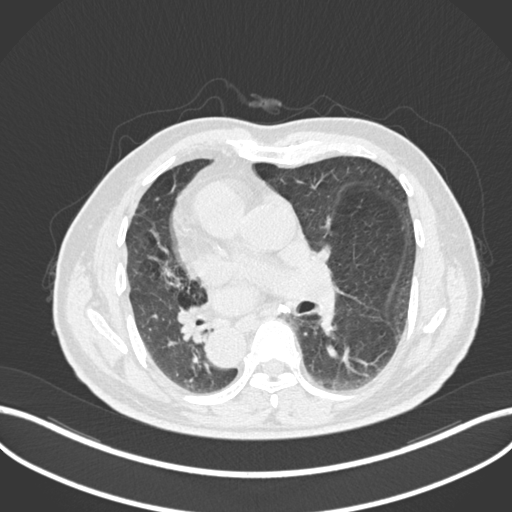
Chest CT, one axial slice. Position 111 of 206 along the scan axis. 120 kVp. Lung window (W 1500 / L -600 HU). 1 mm slice thickness. 512 × 512 image matrix, field of view 400 × 400 mm. Male patient, age 67 years. From the clinical record (not read from this slice): clinical TNM (as recorded): T2a N0 M0.
Structures marked on this image (rectangle marked by the reading radiologist):
- lung tumour (recorded histology: squamous cell carcinoma): bounding box (x1, y1, x2, y2) in pixels: (177, 306, 212, 342)